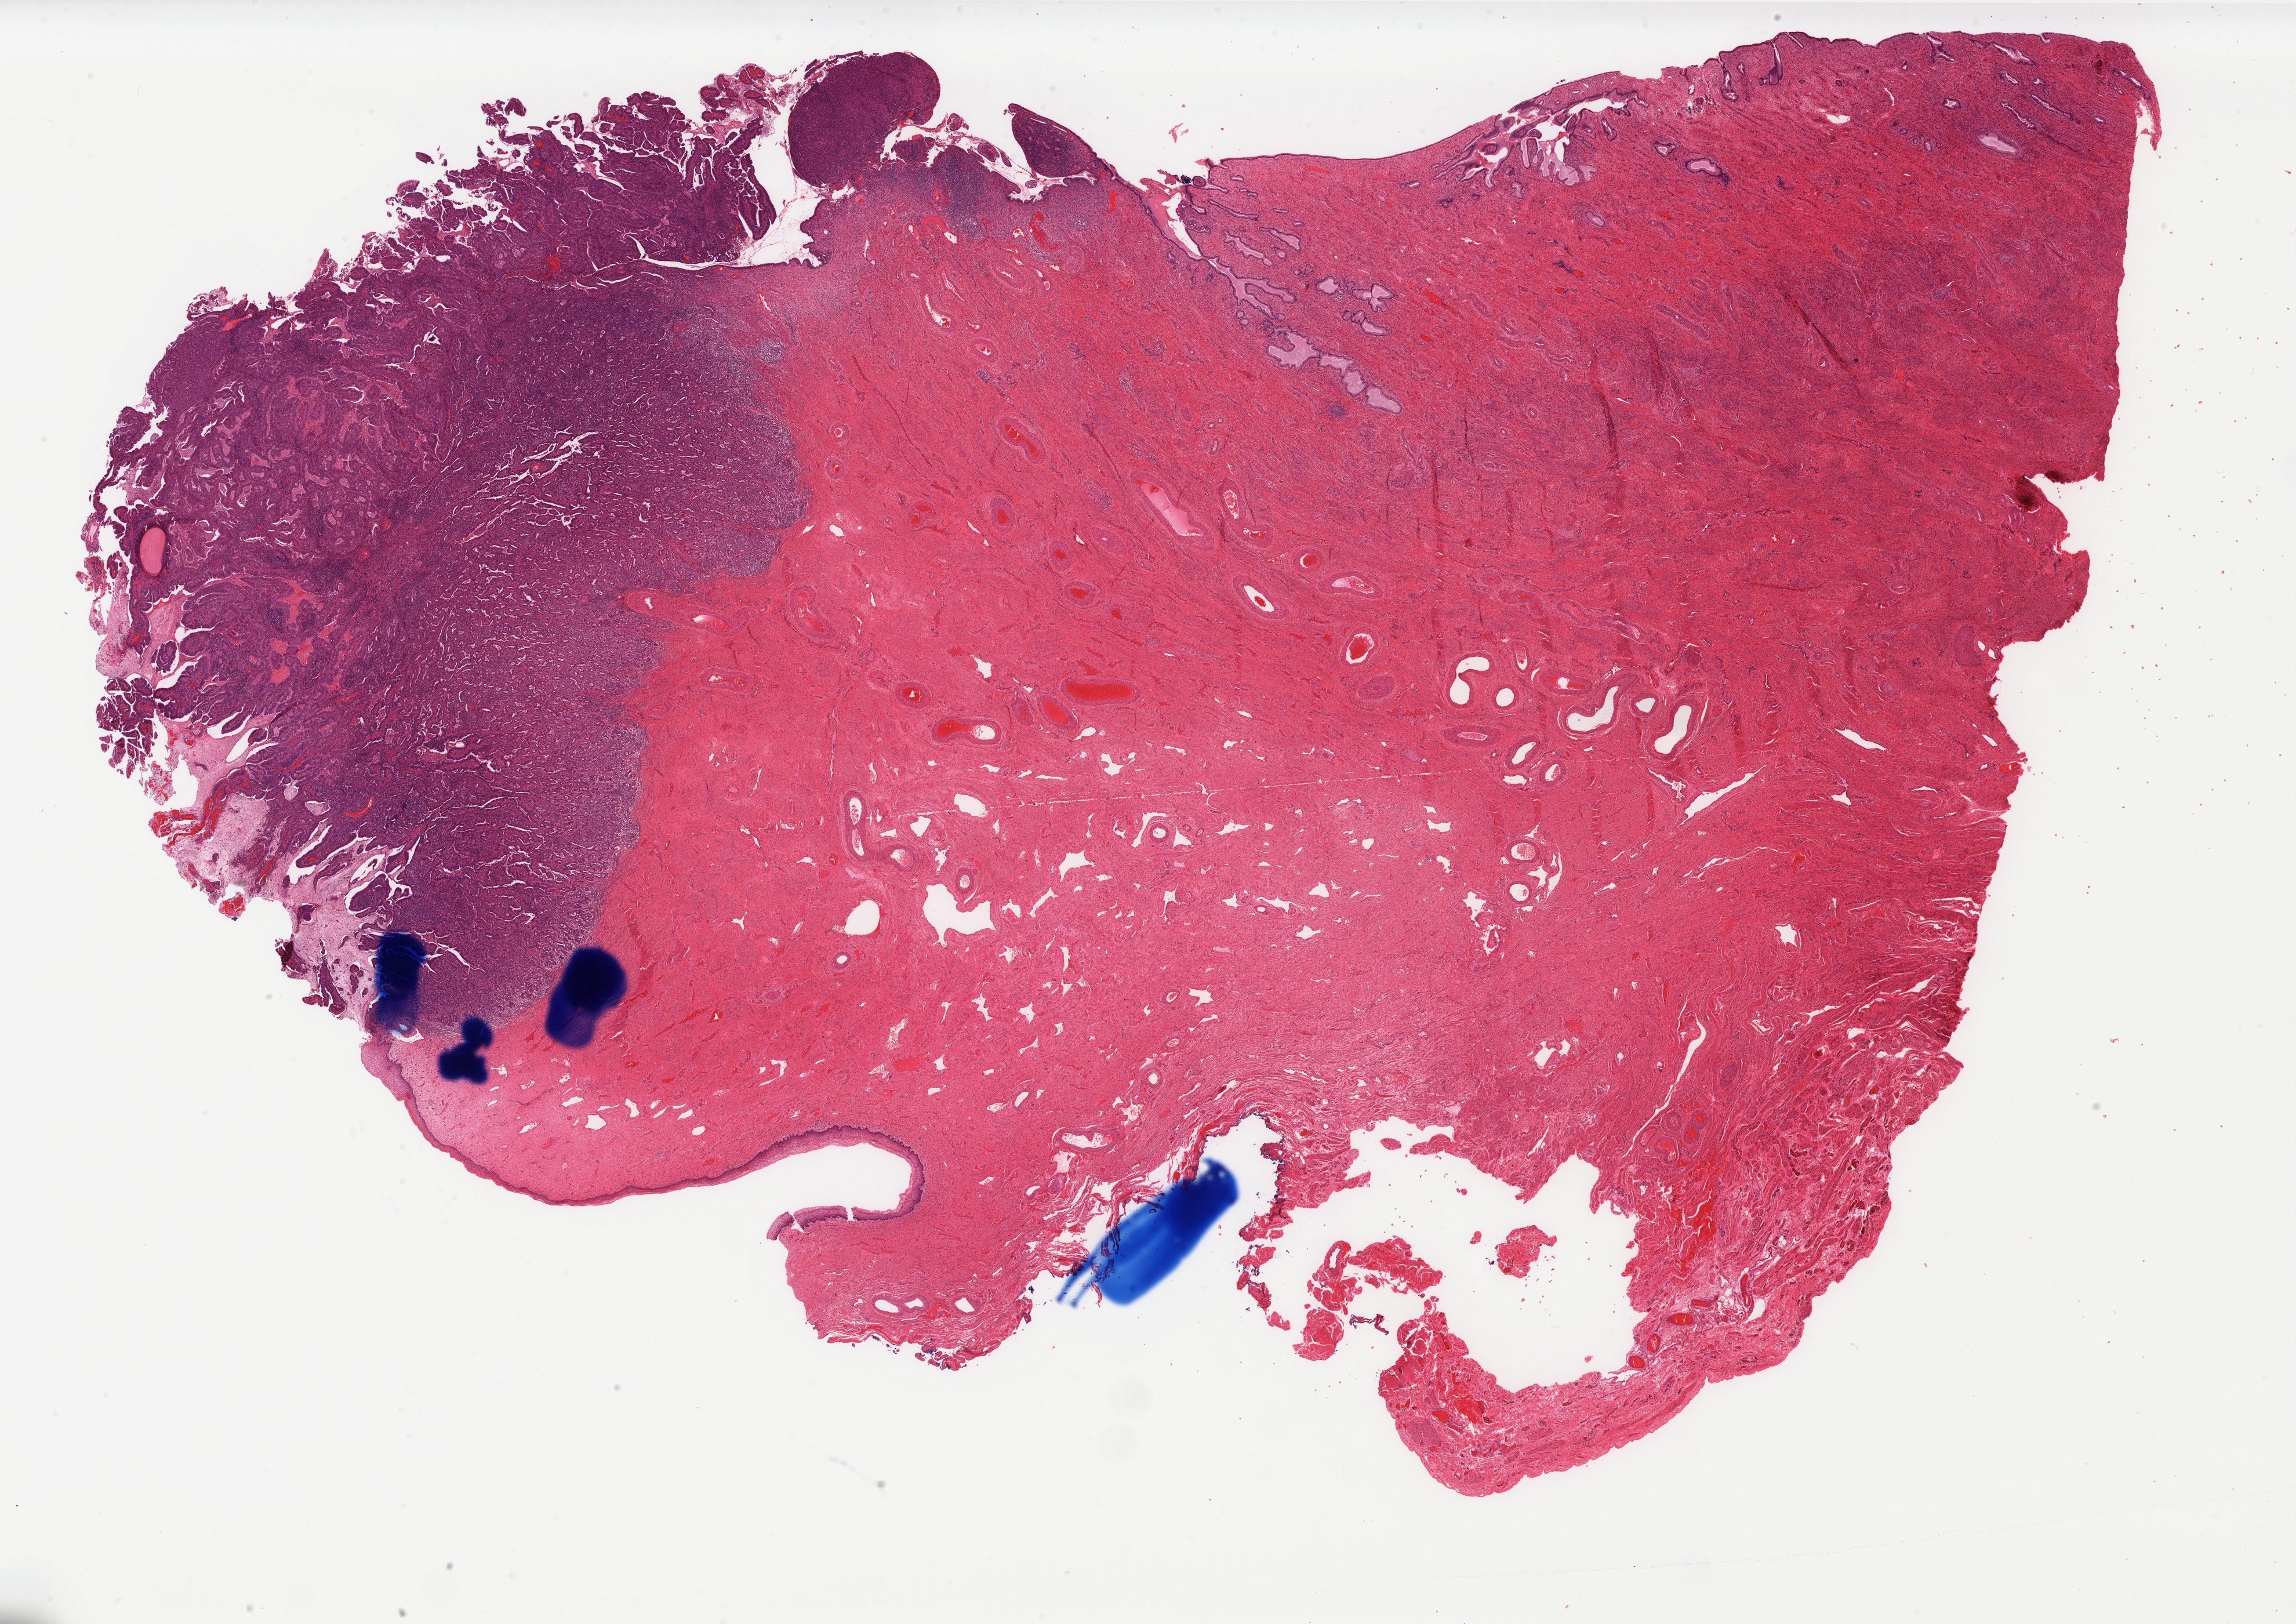
Whole-slide histology image, Hematoxylin and eosin (H&E) stained, low-resolution overview of the scanned area, about 31.7 x 22.4 mm (acquisition: 40x scan). Formalin-fixed paraffin-embedded (FFPE) diagnostic section. Primary tumour sample from the cervix. Patient: female, age at initial diagnosis 37 years. Histologic grade: G2 (moderately differentiated).
Histologic diagnosis: Adenocarcinoma, endocervical type (cervix uteri). Lymph nodes positive (case pathology): 0 of 31 examined. FIGO stage: IB1.